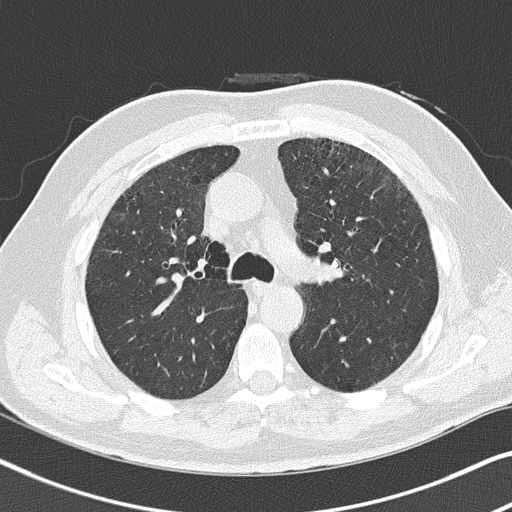
Low-dose screening chest CT, axial slice. First (baseline) screen. Lung window (W 1500 / L -600 HU). 2 mm slice thickness. Lung (sharp) reconstruction kernel (B50f). 120 kVp. Slice 109 of 300 in the series. 512 × 512 image matrix. Male, age 64 years at enrolment. Current smoker at enrolment.
Lesion marked by an expert reader, box from (x=322, y=248) to (x=355, y=277) px. Screening reader's record for this exam (one nodule recorded; not confirmed to be the boxed lesion): non-calcified nodule or mass ≥4 mm, left upper lobe, 4 × 4 mm, smooth margins, soft tissue attenuation. Official screen result: positive, change unspecified: nodule(s) >= 4 mm or enlarging nodule(s), mass(es), or other non-specific abnormalities suspicious for lung cancer. Later outcome: lung cancer diagnosed 450 days after this screen (after the second annual screen) — squamous cell carcinoma, keratinizing, NOS, left upper lobe, moderately differentiated (G2), stage IA (AJCC 6th edition), 4 mm at pathology.